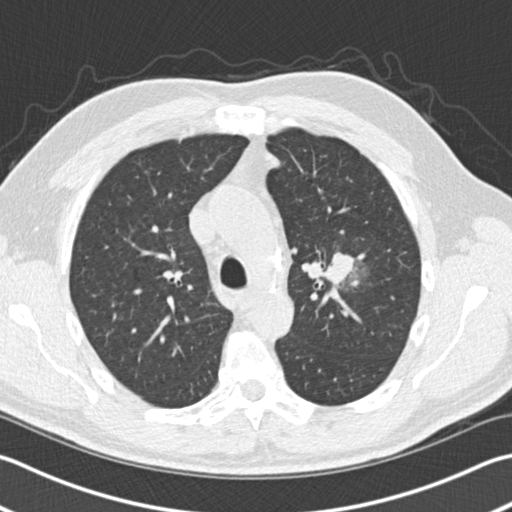
Chest CT (low-dose screening protocol), one axial image, third screening round (two years after baseline), lung window (W 1500 / L -600 HU), 2 mm slice thickness, 512 × 512 image matrix, field of view 346 × 346 mm. Male, age 65 years at enrolment. Former smoker at enrolment.
- Expert reader's lesion annotation, bounding box <306,240,370,304> (left, top, right, bottom; pixels).
- The screening reader recorded 4 non-calcified nodules or masses ≥4 mm on this exam (left upper lobe, left upper lobe, left lower lobe, right middle lobe); which of them this box marks is not recorded.
- Official screen result: positive, other.